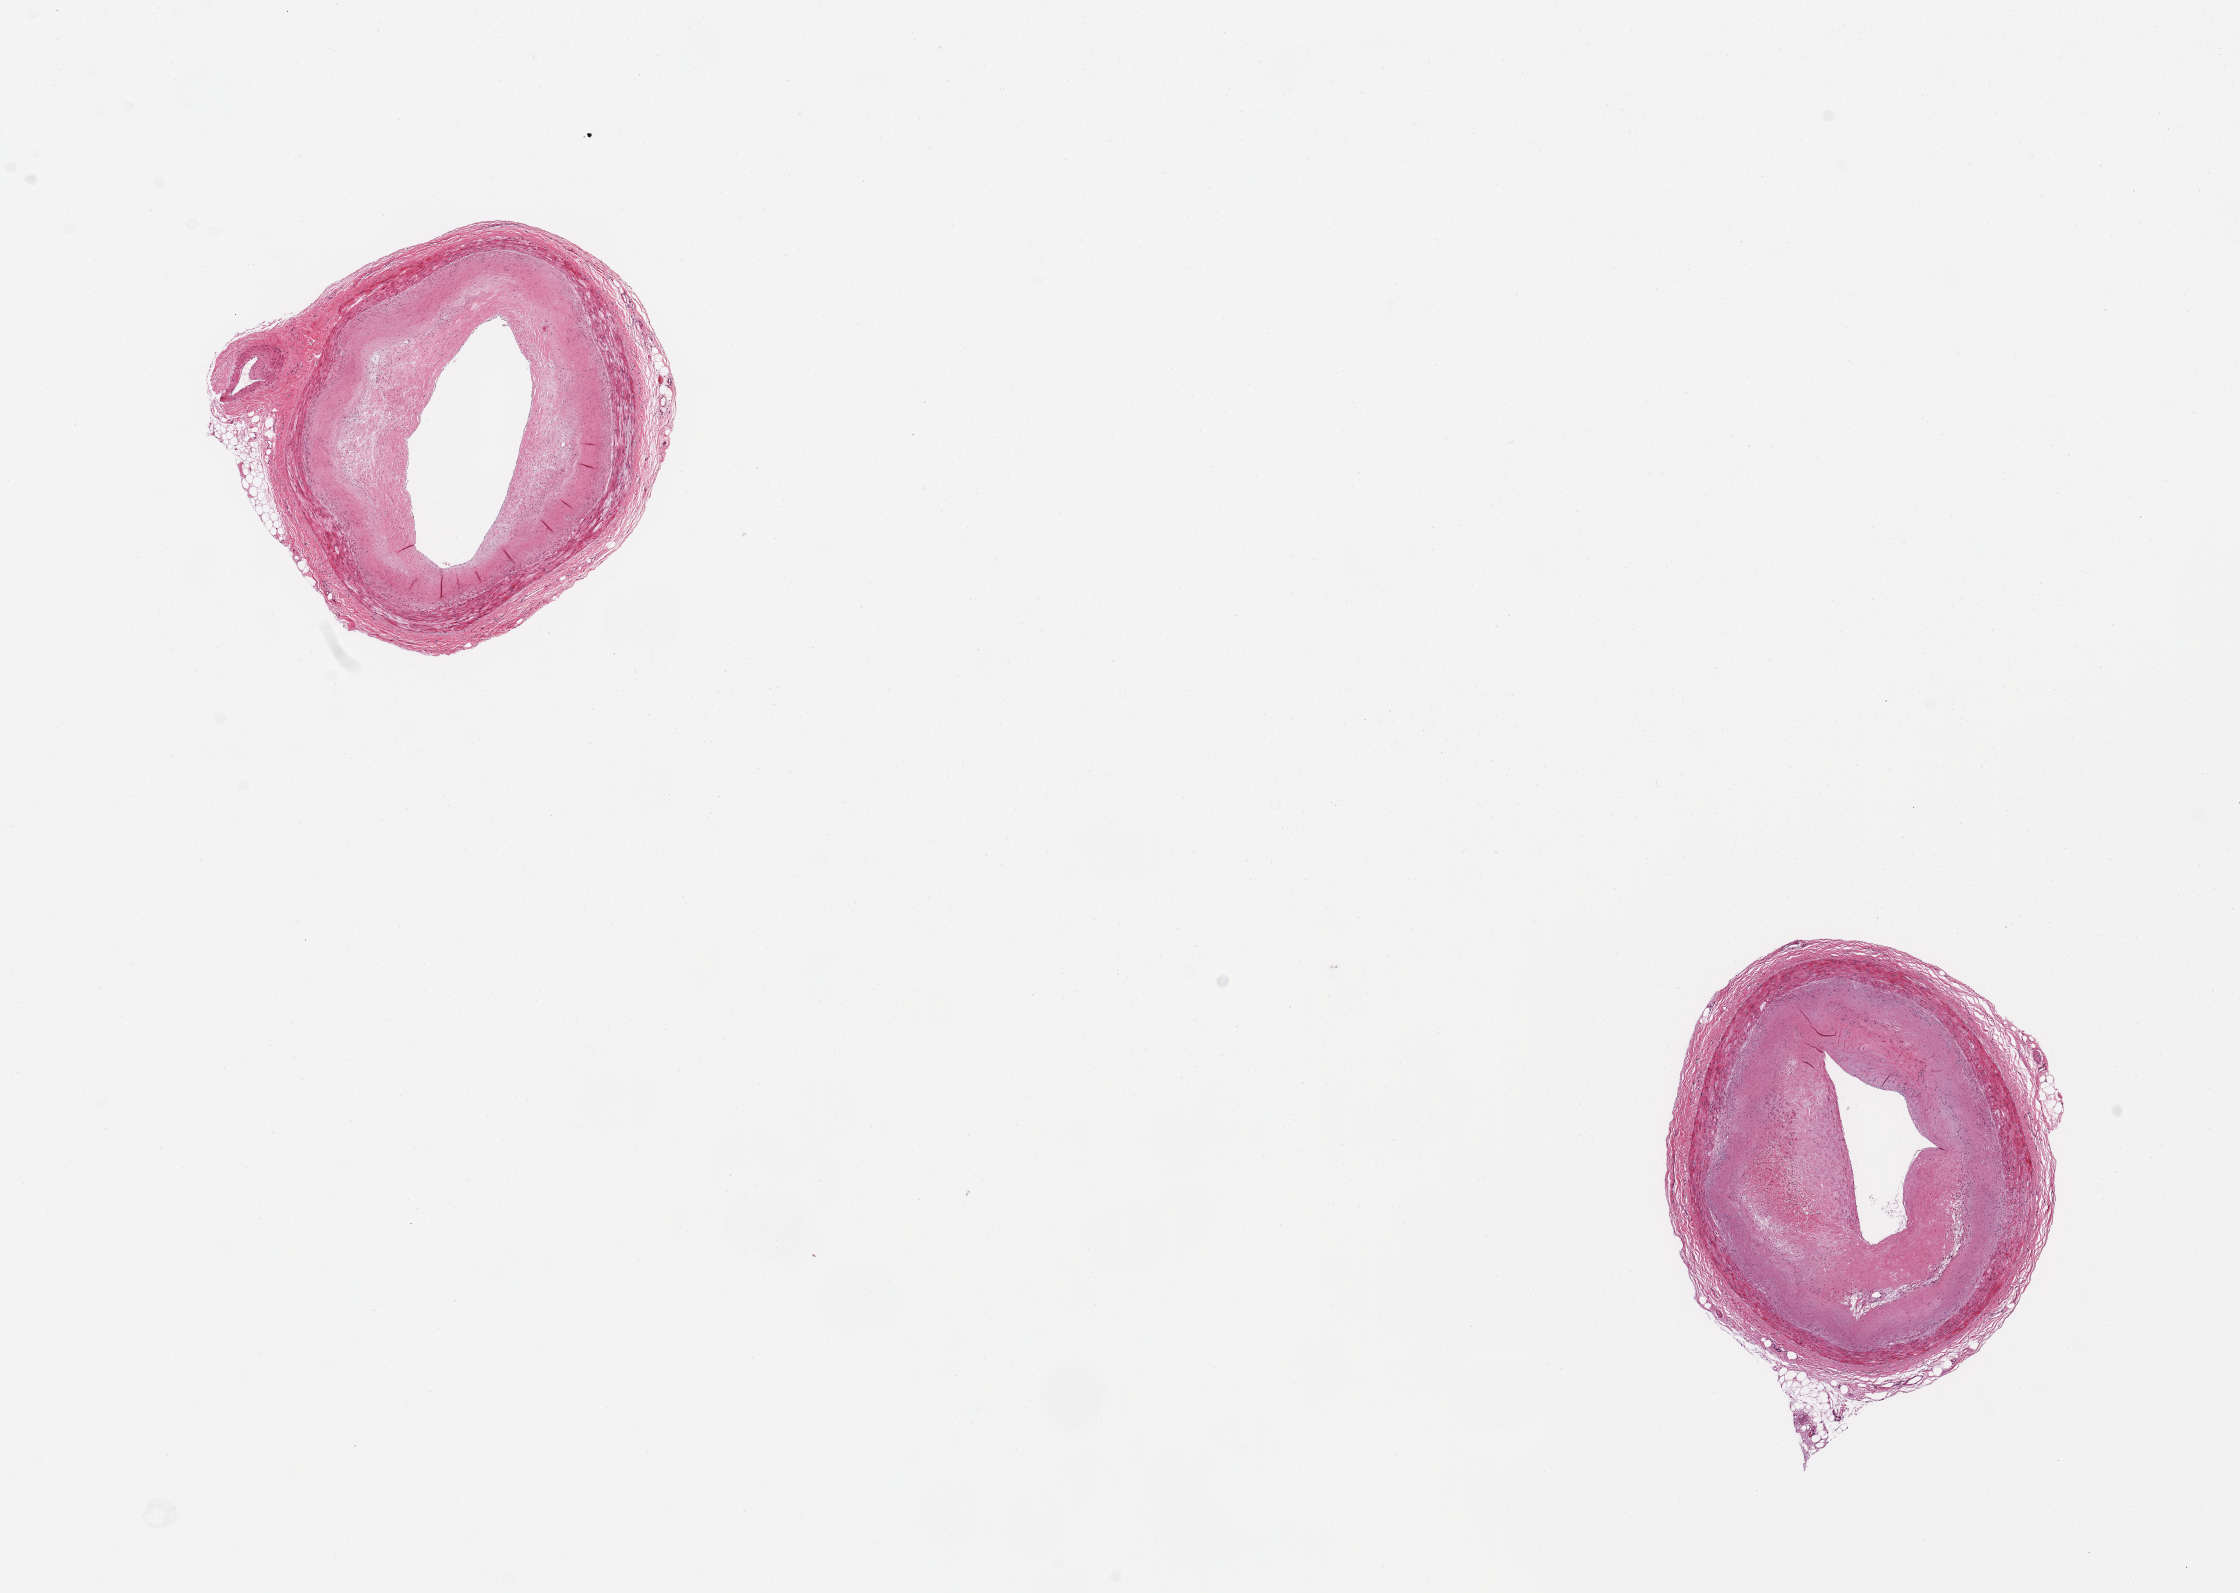
H&E whole-slide image, low-resolution overview of the scanned area, about 17.7 x 12.6 mm (slide scanned at 20x); PAXgene-fixed paraffin-embedded (PFPE) section; sampled site (target tissue): coronary artery; tissue donor sample. Donor: male.
* review note (as recorded): 2 ~3.5mm sections, ~50-60% occlusive atherosclerosis